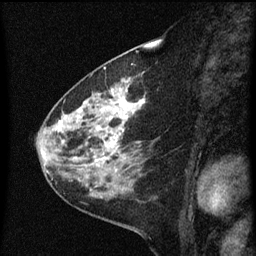
Breast MRI (dynamic contrast-enhanced), one sagittal slice; slice 24 of 60 in the series (ordered by position); dynamic contrast-enhanced series, image 2 of 3 at this slice position (ordered by acquisition); 1.5 T; TE 4.2 ms, TR 8 ms; 2 mm slice thickness; 256 × 256 image matrix, field of view 180 × 180 mm. Patient: female, 60 years.
Structures marked on this image (semi-automatic segmentation, software-assisted and operator-edited):
- analysis volume of interest (the breast-tissue region the enhancement analysis was run in; not a lesion): box from (x=48, y=82) to (x=149, y=183) px
- tumour enhancement mask (voxels above the 70 % enhancement threshold inside the analysis volume of interest): (x=58, y=82)–(x=142, y=163)